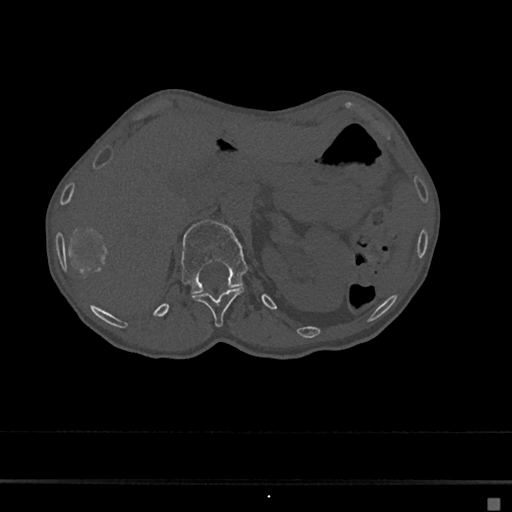
CT including the spine, one axial slice; slice 90 of 797 in the series (ordered by position); reconstruction kernel Br40s/3; 120 kVp; bone window (W 1800 / L 400 HU); 0.5 mm slice thickness; 512 × 512 image matrix, field of view 360 × 360 mm. Patient: female, 68 years. From the clinical record (not read from this slice): primary cancer: renal.
Outlined on this slice (semi-automatically segmented with operator editing):
- L1 vertebra: bounding box [x1, y1, x2, y2] px = [181, 220, 248, 294]
- T12 vertebra: [192, 288, 244, 327]